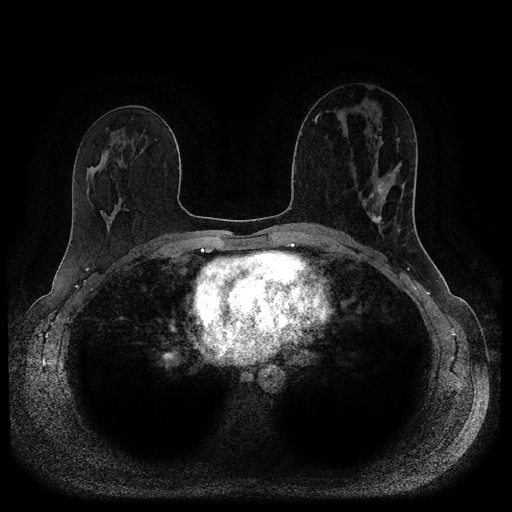
Breast MRI (dynamic contrast-enhanced, multi-phase), one axial slice. Position 54 of 116 along the scan axis. Dynamic contrast-enhanced series, time point 2 of 5 at this slice position (early post-contrast). 1.5 T. TE 2.6 ms, TR 5.3 ms. 2 mm slice thickness. 512 × 512 image matrix, field of view 350 × 350 mm. Female patient, age 45 years.
Annotated regions visible in this slice (semi-automatically segmented with operator editing):
- breast lesion (labelled 'tumour' in the annotation; benign lesions carry a separate 'benign' label): bounding box <366,182,386,225> (left, top, right, bottom; pixels)